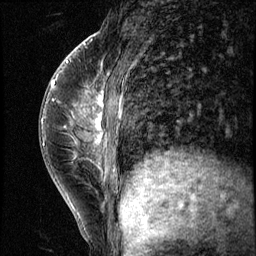
Breast MRI (dynamic contrast-enhanced), one sagittal slice. Slice 21 of 56 in the series (ordered by position). 3 images stored at this slice position (order not interpretable as contrast timing). 1.5 T. TE 4.2 ms, TR 8.7 ms. 256 × 256 image matrix, field of view 180 × 180 mm. Female patient, age 35 years. From the clinical record (not read from this slice): setting: breast cancer imaged before/during neoadjuvant chemotherapy; receptor status: HER2-positive.
Outlined on this slice (semi-automatic segmentation, software-assisted and operator-edited):
- analysis volume of interest (the breast-tissue region the enhancement analysis was run in; not a lesion): bounding box [x1, y1, x2, y2] px = [58, 84, 138, 186]
- tumour enhancement mask (voxels above the 140 % enhancement threshold inside the analysis volume of interest): [92, 87, 122, 172]